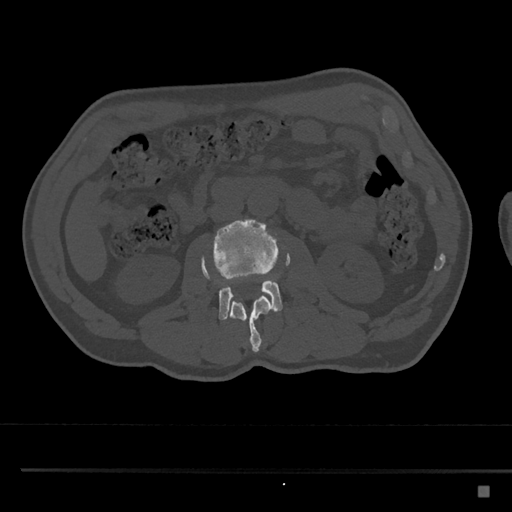
CT including the spine, one axial slice. Position 726 of 797 along the scan axis. Reconstruction kernel Br40s/3. 120 kVp. Bone window (W 1800 / L 400 HU). 512 × 512 image matrix, field of view 391 × 391 mm. Patient: male, 59 years. Case-level facts recorded for this patient, not image findings: primary cancer: prostate.
Outlined on this slice (semi-automatically segmented with operator editing):
- L2 vertebra: box from (x=202, y=257) to (x=273, y=352) px
- L3 vertebra: (x=201, y=219)–(x=291, y=320)